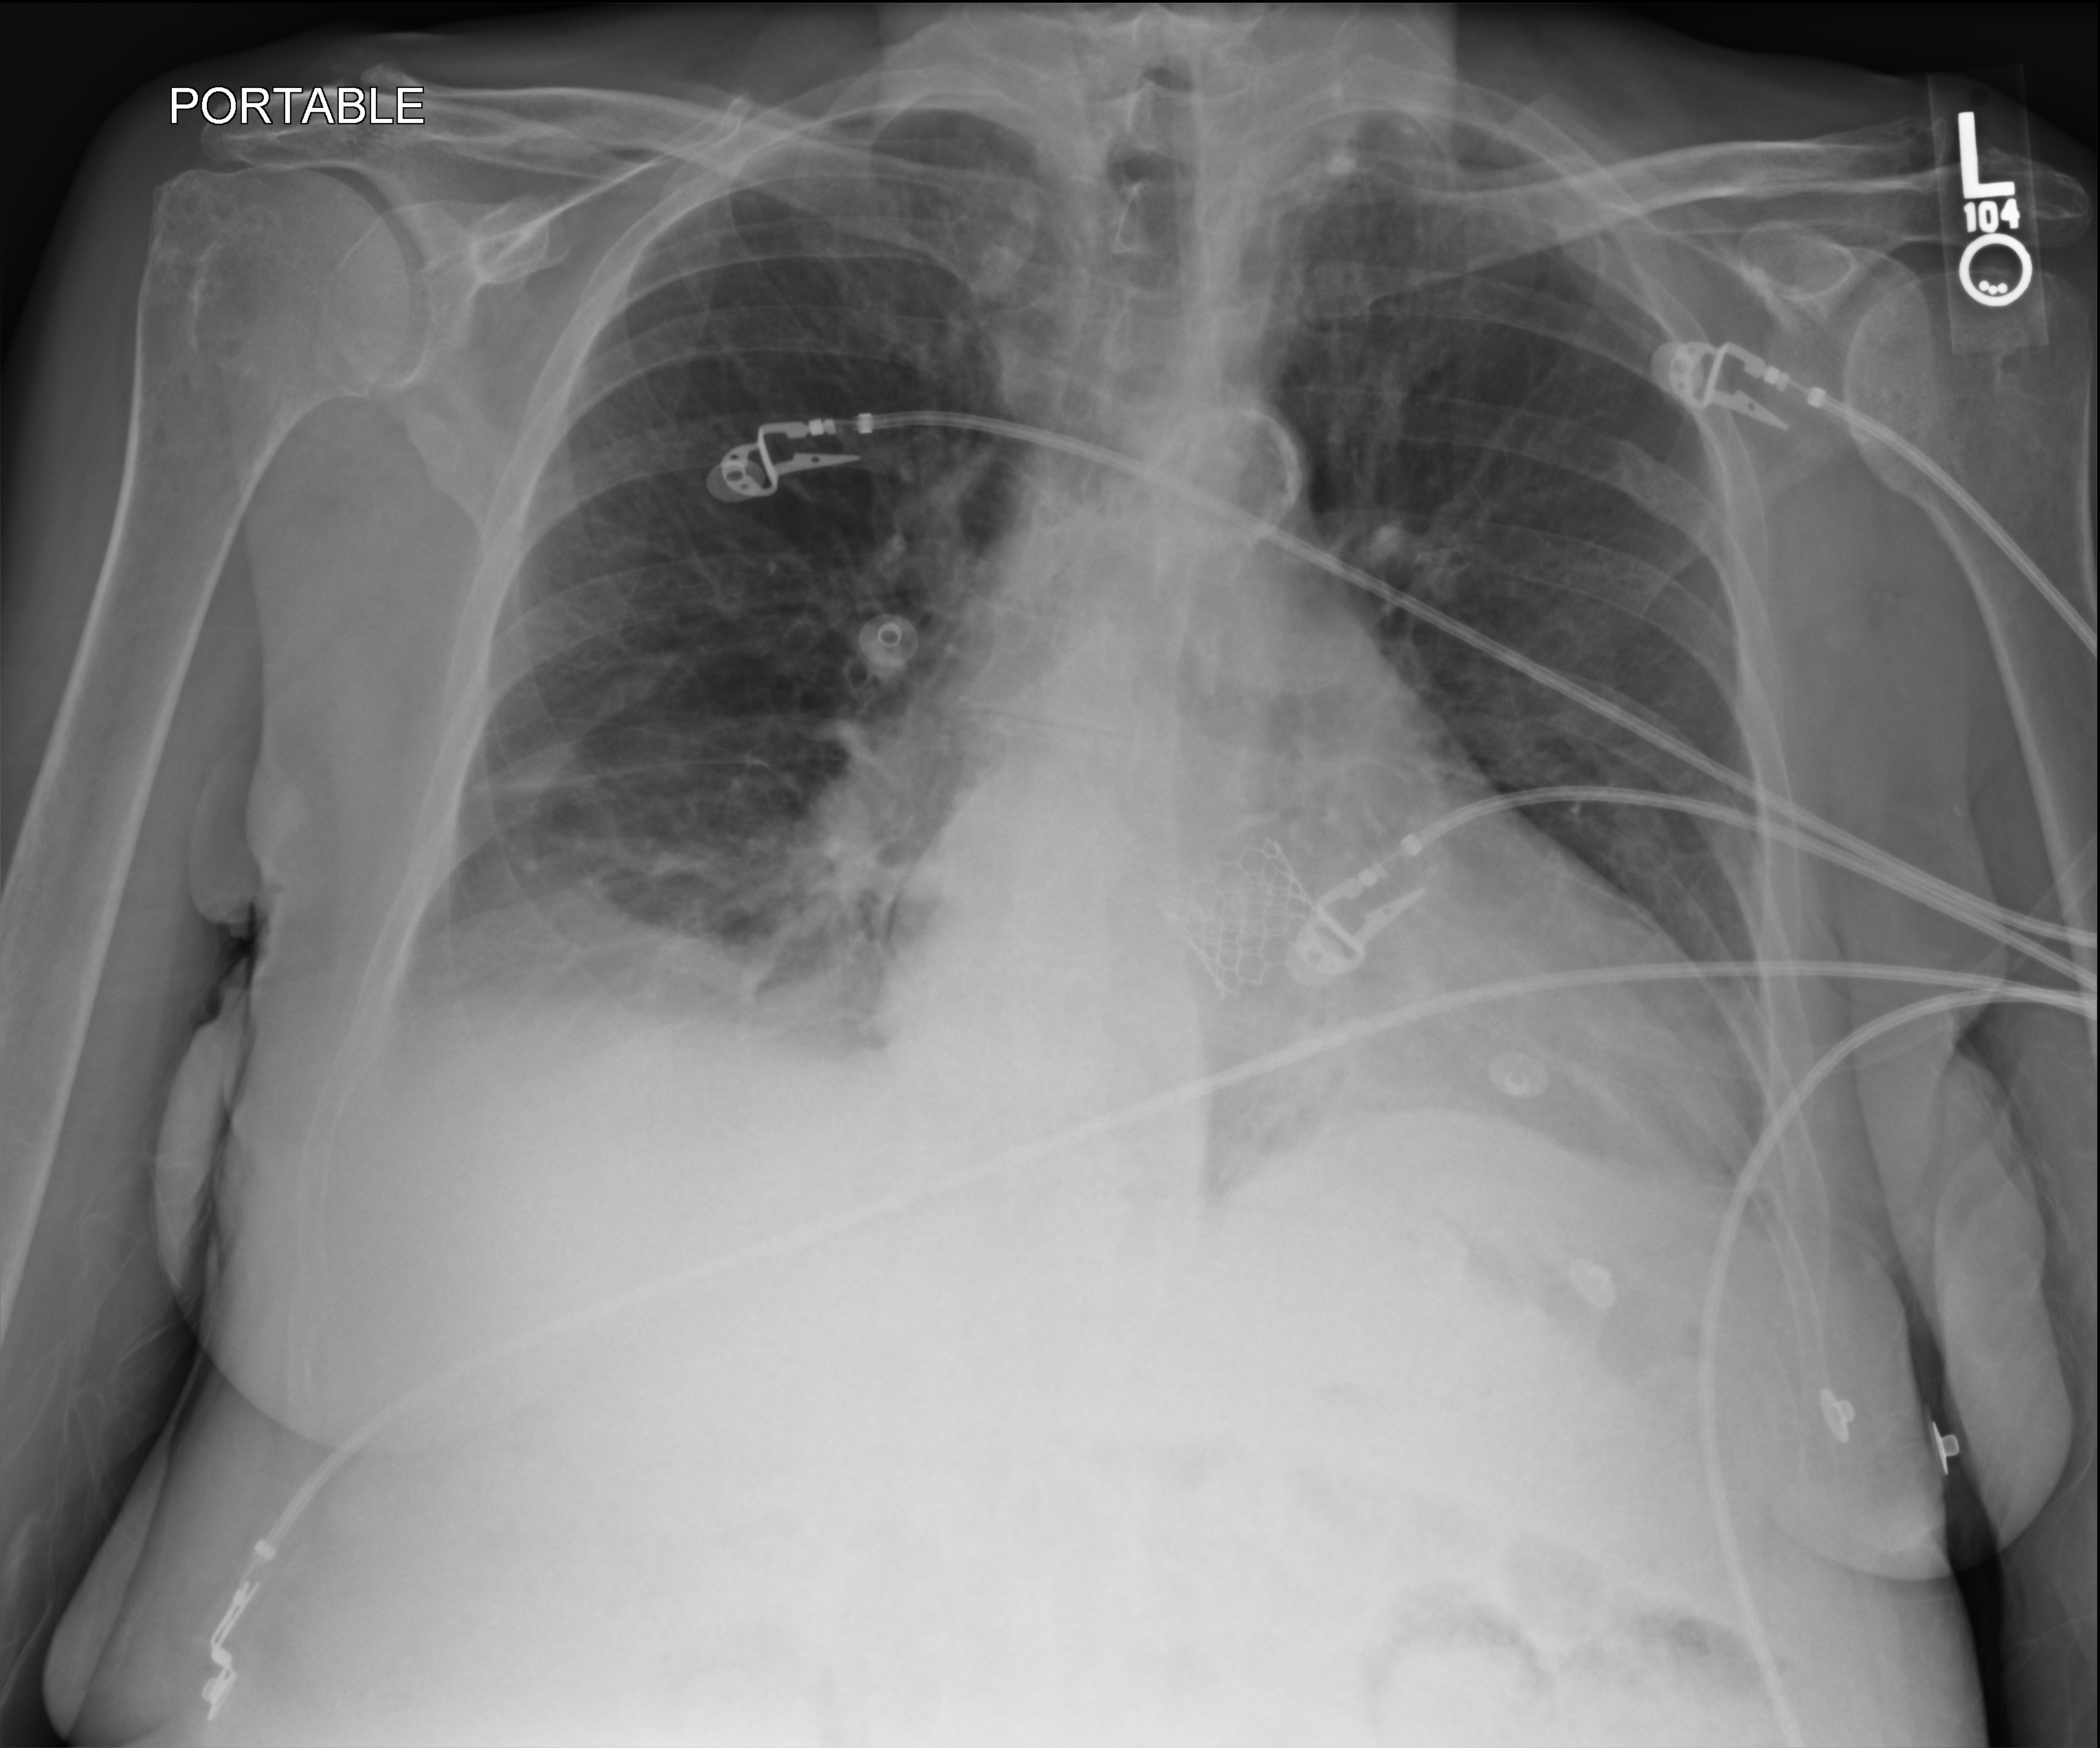
Chest X-ray (portable), anteroposterior (AP) projection. Female patient hospitalised with COVID-19, age 75–90 years.
Hospital-stay facts (about this admission, not read from this image; timing relative to this image not recorded):
- admitted to intensive care during this hospital stay: no
- COPD (admission record): yes